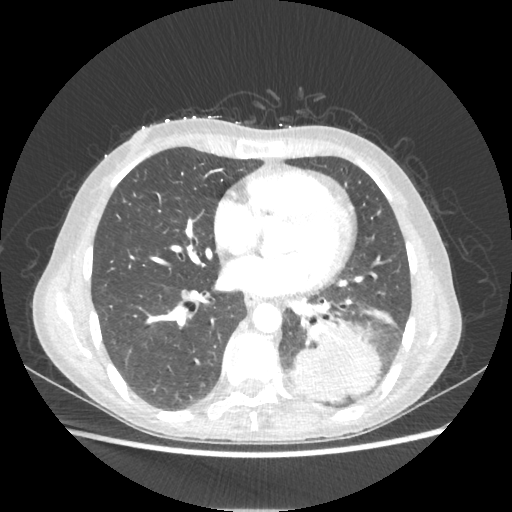
Chest CT, one axial slice. Position 96 of 221 along the scan axis. Reconstruction kernel STANDARD. 80 kVp. Lung window (W 1500 / L -600 HU). 512 × 512 image matrix, field of view 360 × 360 mm. Patient: female, 53 years. From the clinical record (not read from this slice): clinical TNM (as recorded): T3 N0 M0.
Annotated regions visible in this slice (rectangle marked by the reading radiologist):
- lung tumour (recorded histology: adenocarcinoma): bounding box (x1, y1, x2, y2) in pixels: (286, 321, 380, 402)